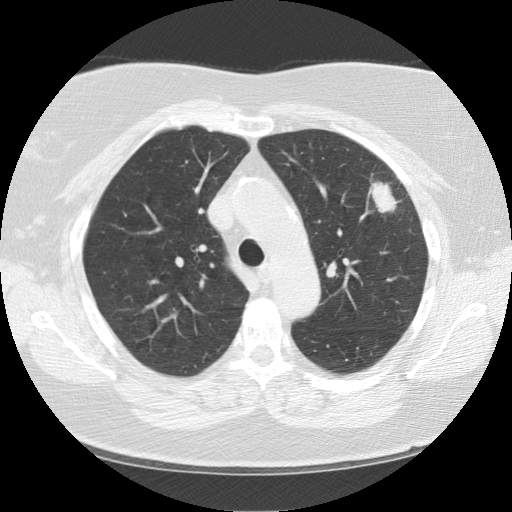
Low-dose screening chest CT, one axial slice; slice 94 of 130 in the series (ordered by position); lung window (W 1500 / L -600 HU); 2.5 mm slice thickness; 512 × 512 image matrix, field of view 350 × 350 mm.
Annotated regions visible in this slice (manually delineated by an expert):
- lesion 1 (tumor, upper lobe of left lung): bounding box (x1, y1, x2, y2) in pixels: (368, 182, 401, 213)